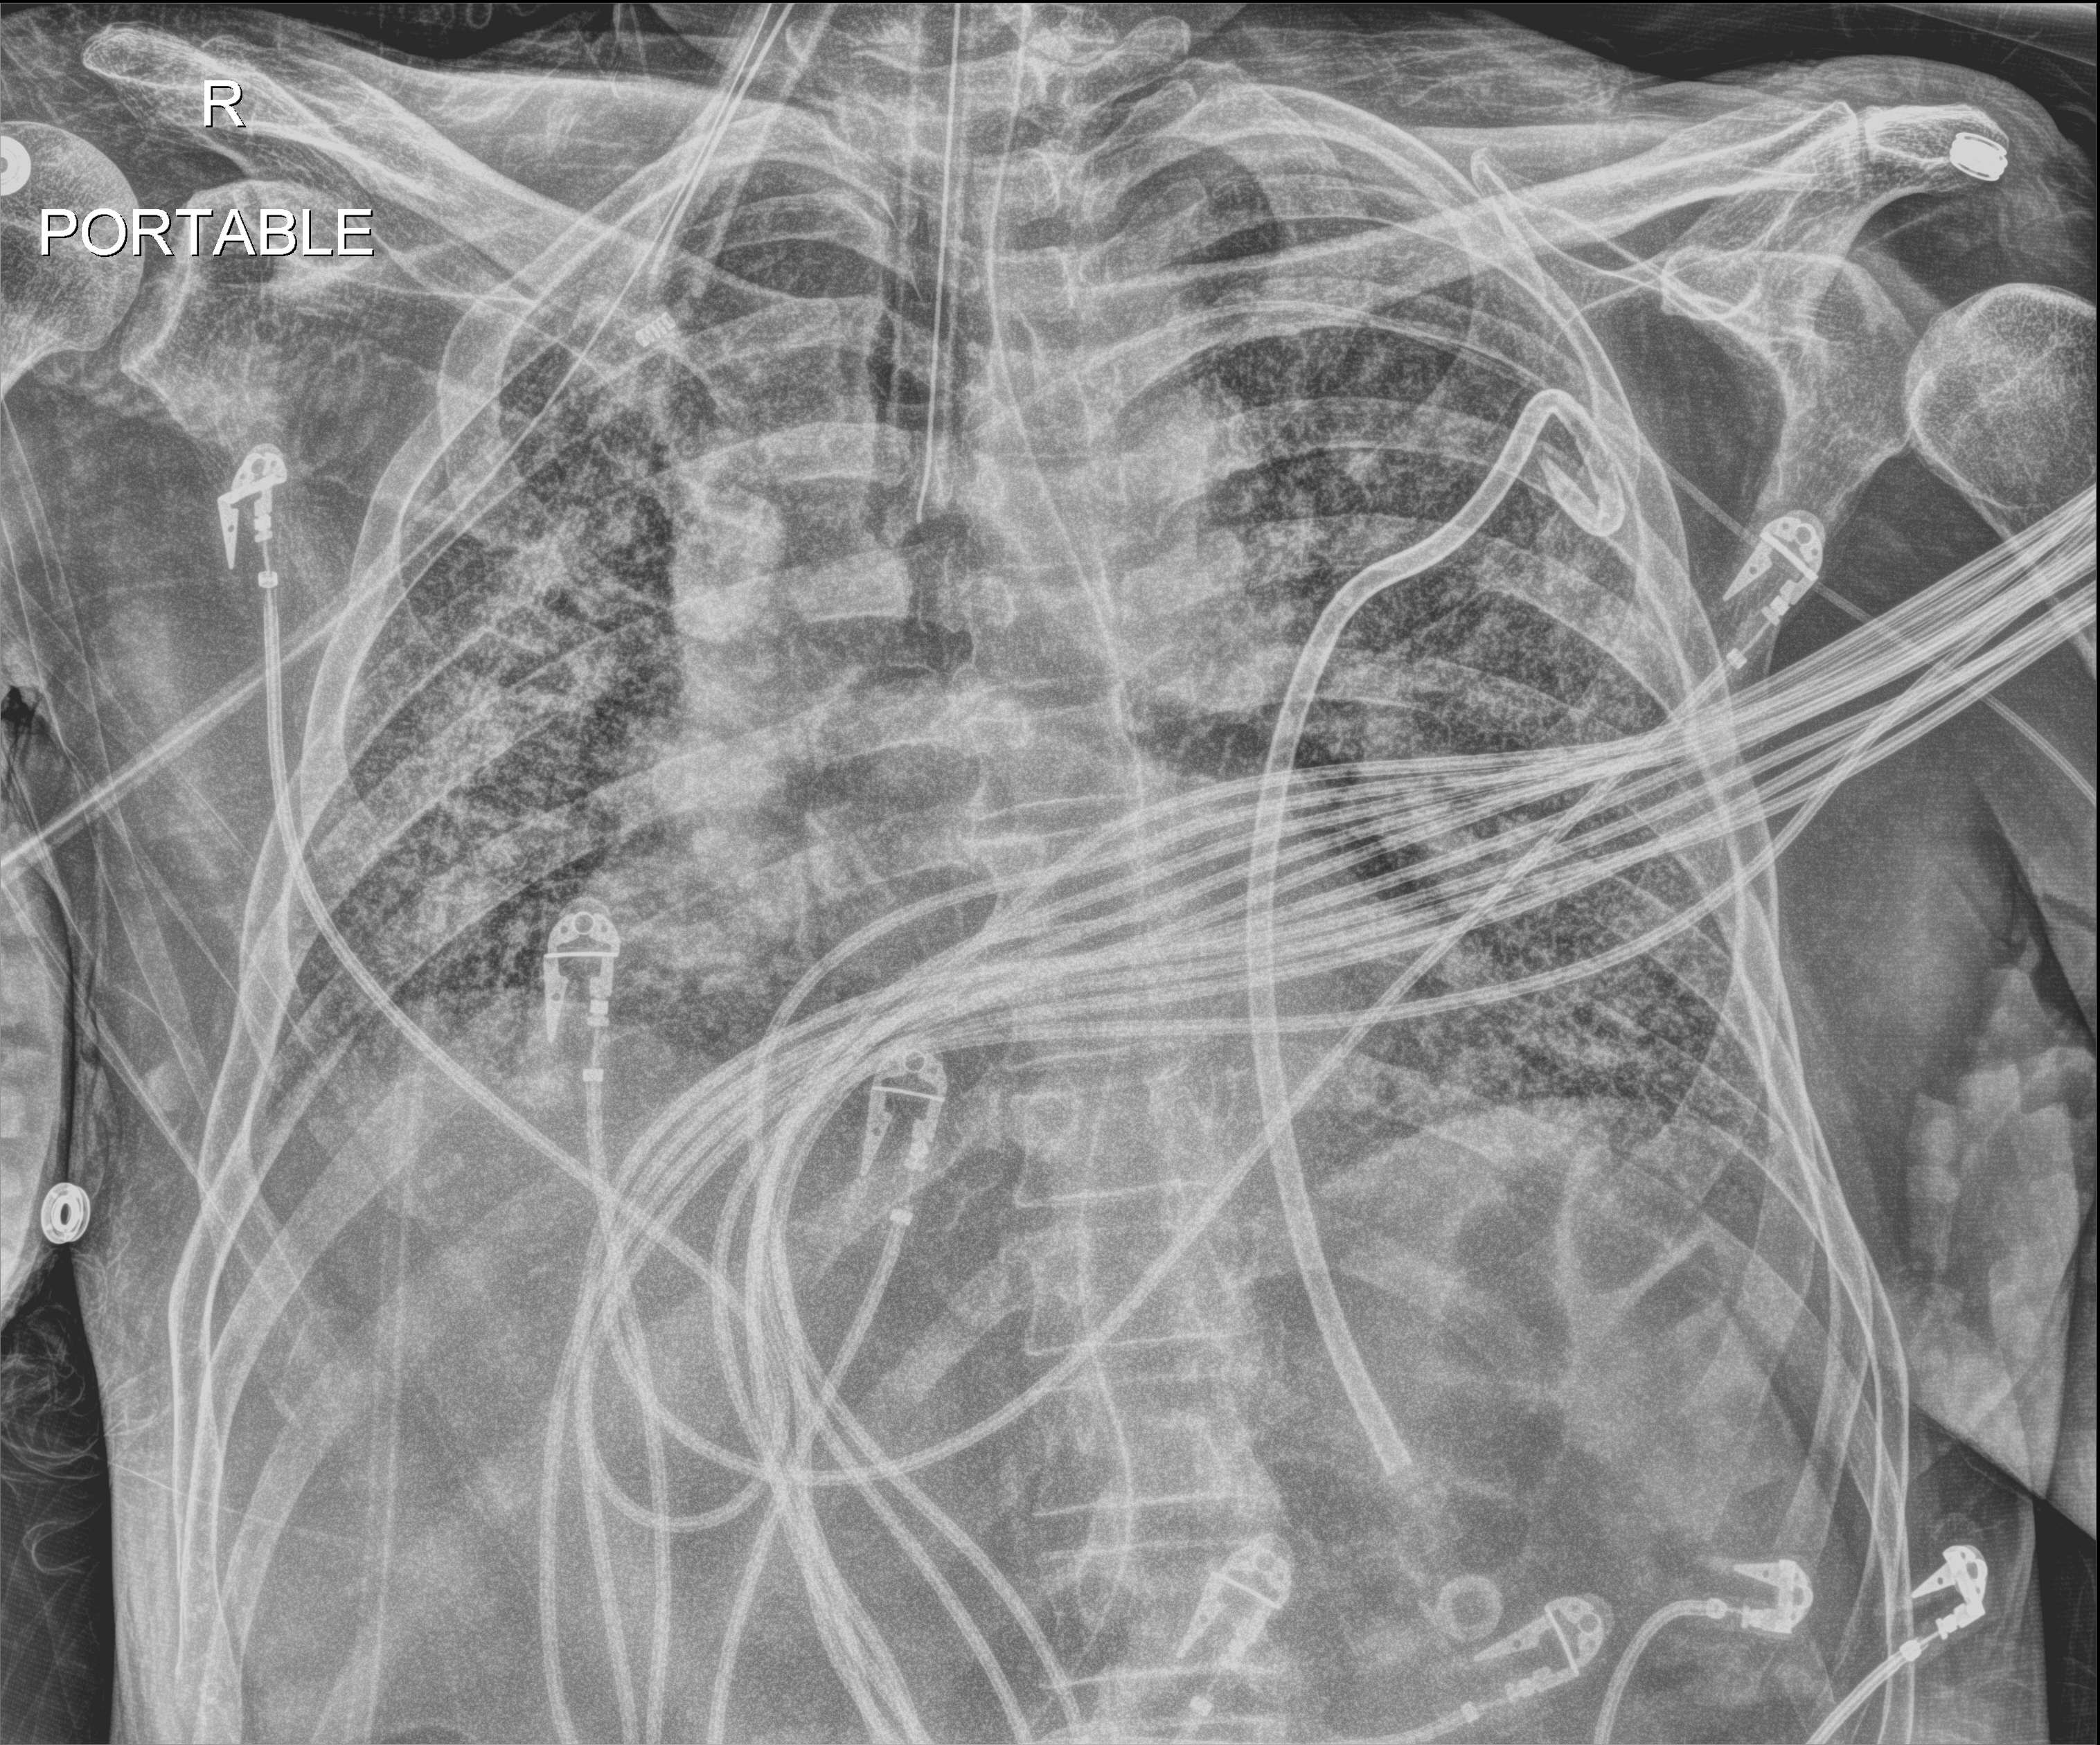
Chest X-ray. Male patient hospitalised with COVID-19, age 60–74 years.
Admission-level facts for this patient (not findings on this image; timing relative to this image not recorded):
- length of hospital stay: 54 days
- admitted to intensive care during this hospital stay: yes
- mechanically ventilated during this hospital stay: yes